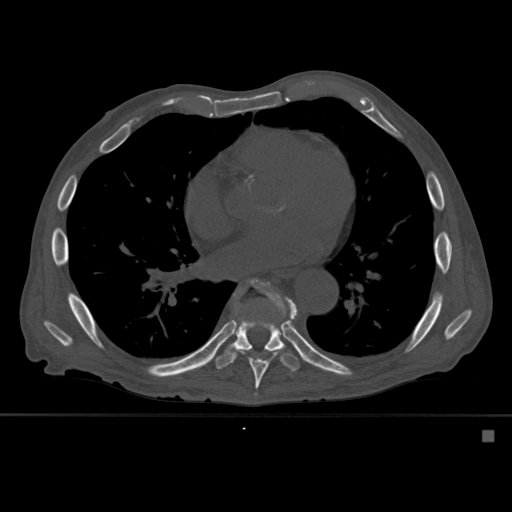
CT including the spine, one axial slice. Position 342 of 527 along the scan axis. Bone window (W 1800 / L 400 HU). 1.5 mm slice thickness. 512 × 512 image matrix. Male patient, age 78 years. Case-level facts recorded for this patient, not image findings: primary cancer: prostate.
Outlined on this slice (semi-automatic segmentation, software-assisted and operator-edited):
- T8 vertebra: bounding box <234,279,297,397> (left, top, right, bottom; pixels)
- T9 vertebra: <213,283,304,372>